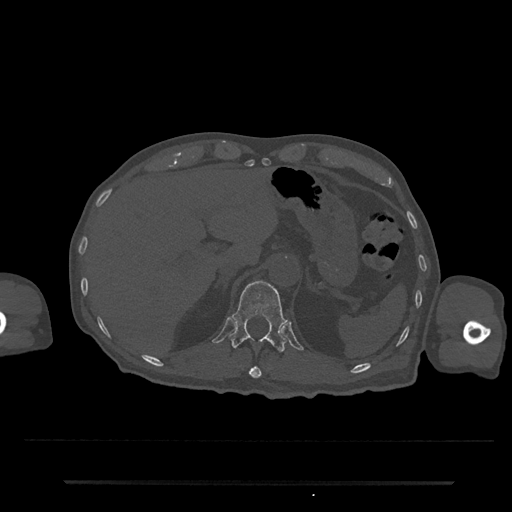
CT including the spine, one axial slice; position 207 of 797 along the scan axis; reconstruction kernel Br40s/3; 120 kVp; bone window (W 1800 / L 400 HU); 0.5 mm slice thickness; 512 × 512 image matrix. Male patient, age 74 years. From the clinical record (not read from this slice): primary cancer: prostate.
Structures marked on this image (semi-automatically segmented with operator editing):
- T11 vertebra: box from (x=249, y=366) to (x=262, y=379) px
- T12 vertebra: (x=229, y=280)–(x=287, y=352)